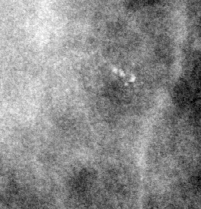
Region of interest cut from a scanned film mammogram (one marked finding), right breast, CC view, BI-RADS breast density category 4 (scale 1–4).
Marked abnormality: calcifications, morphology pleomorphic, distribution clustered; BI-RADS assessment category 4; pathology result (as recorded, not read from the image): benign.